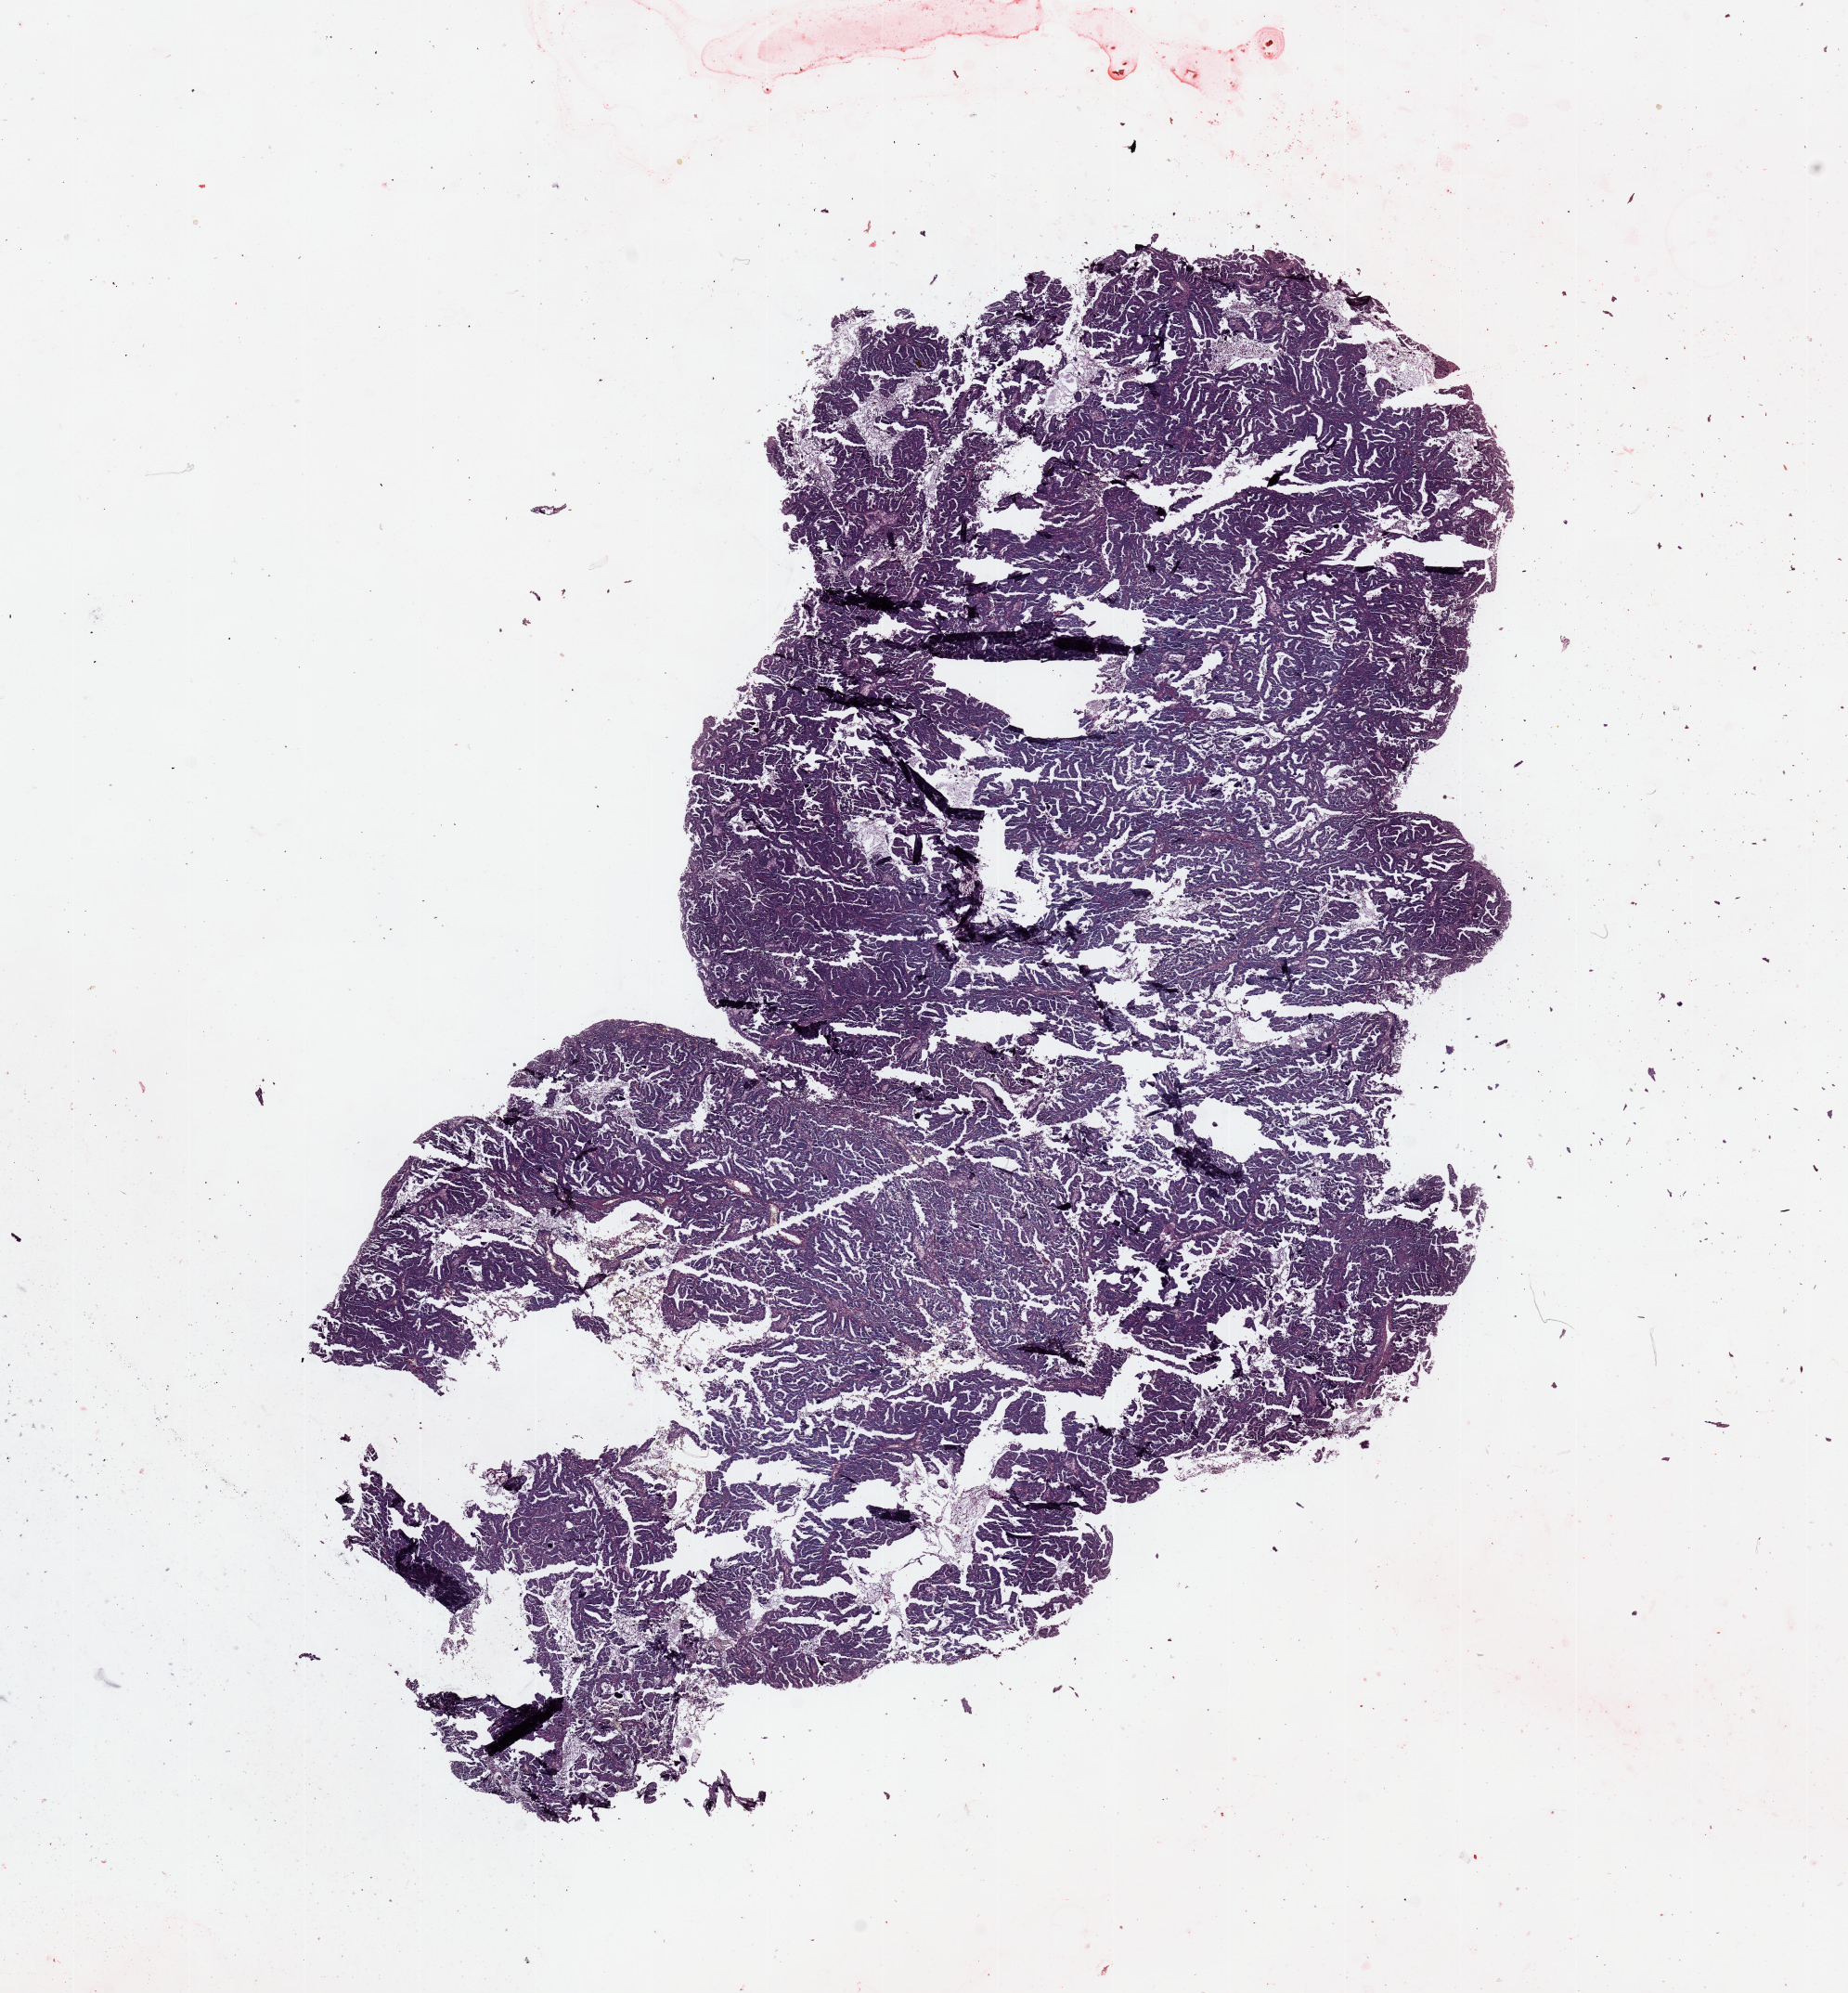
Digitized Hematoxylin and eosin (H&E) stained tissue section (whole slide), a low-resolution overview of the entire scanned area, about 15.8 x 17.0 mm (acquisition: 20x scan), tumour tissue sample, sampled site: uterus. Patient: female, age 70 years. Histologic grade: G2 (moderately differentiated). Pathologist review of this section (percent, as recorded): tumour nuclei 95%, necrosis 2%.
• diagnosis: Endometrioid adenocarcinoma, NOS
• AJCC pathologic stage: I